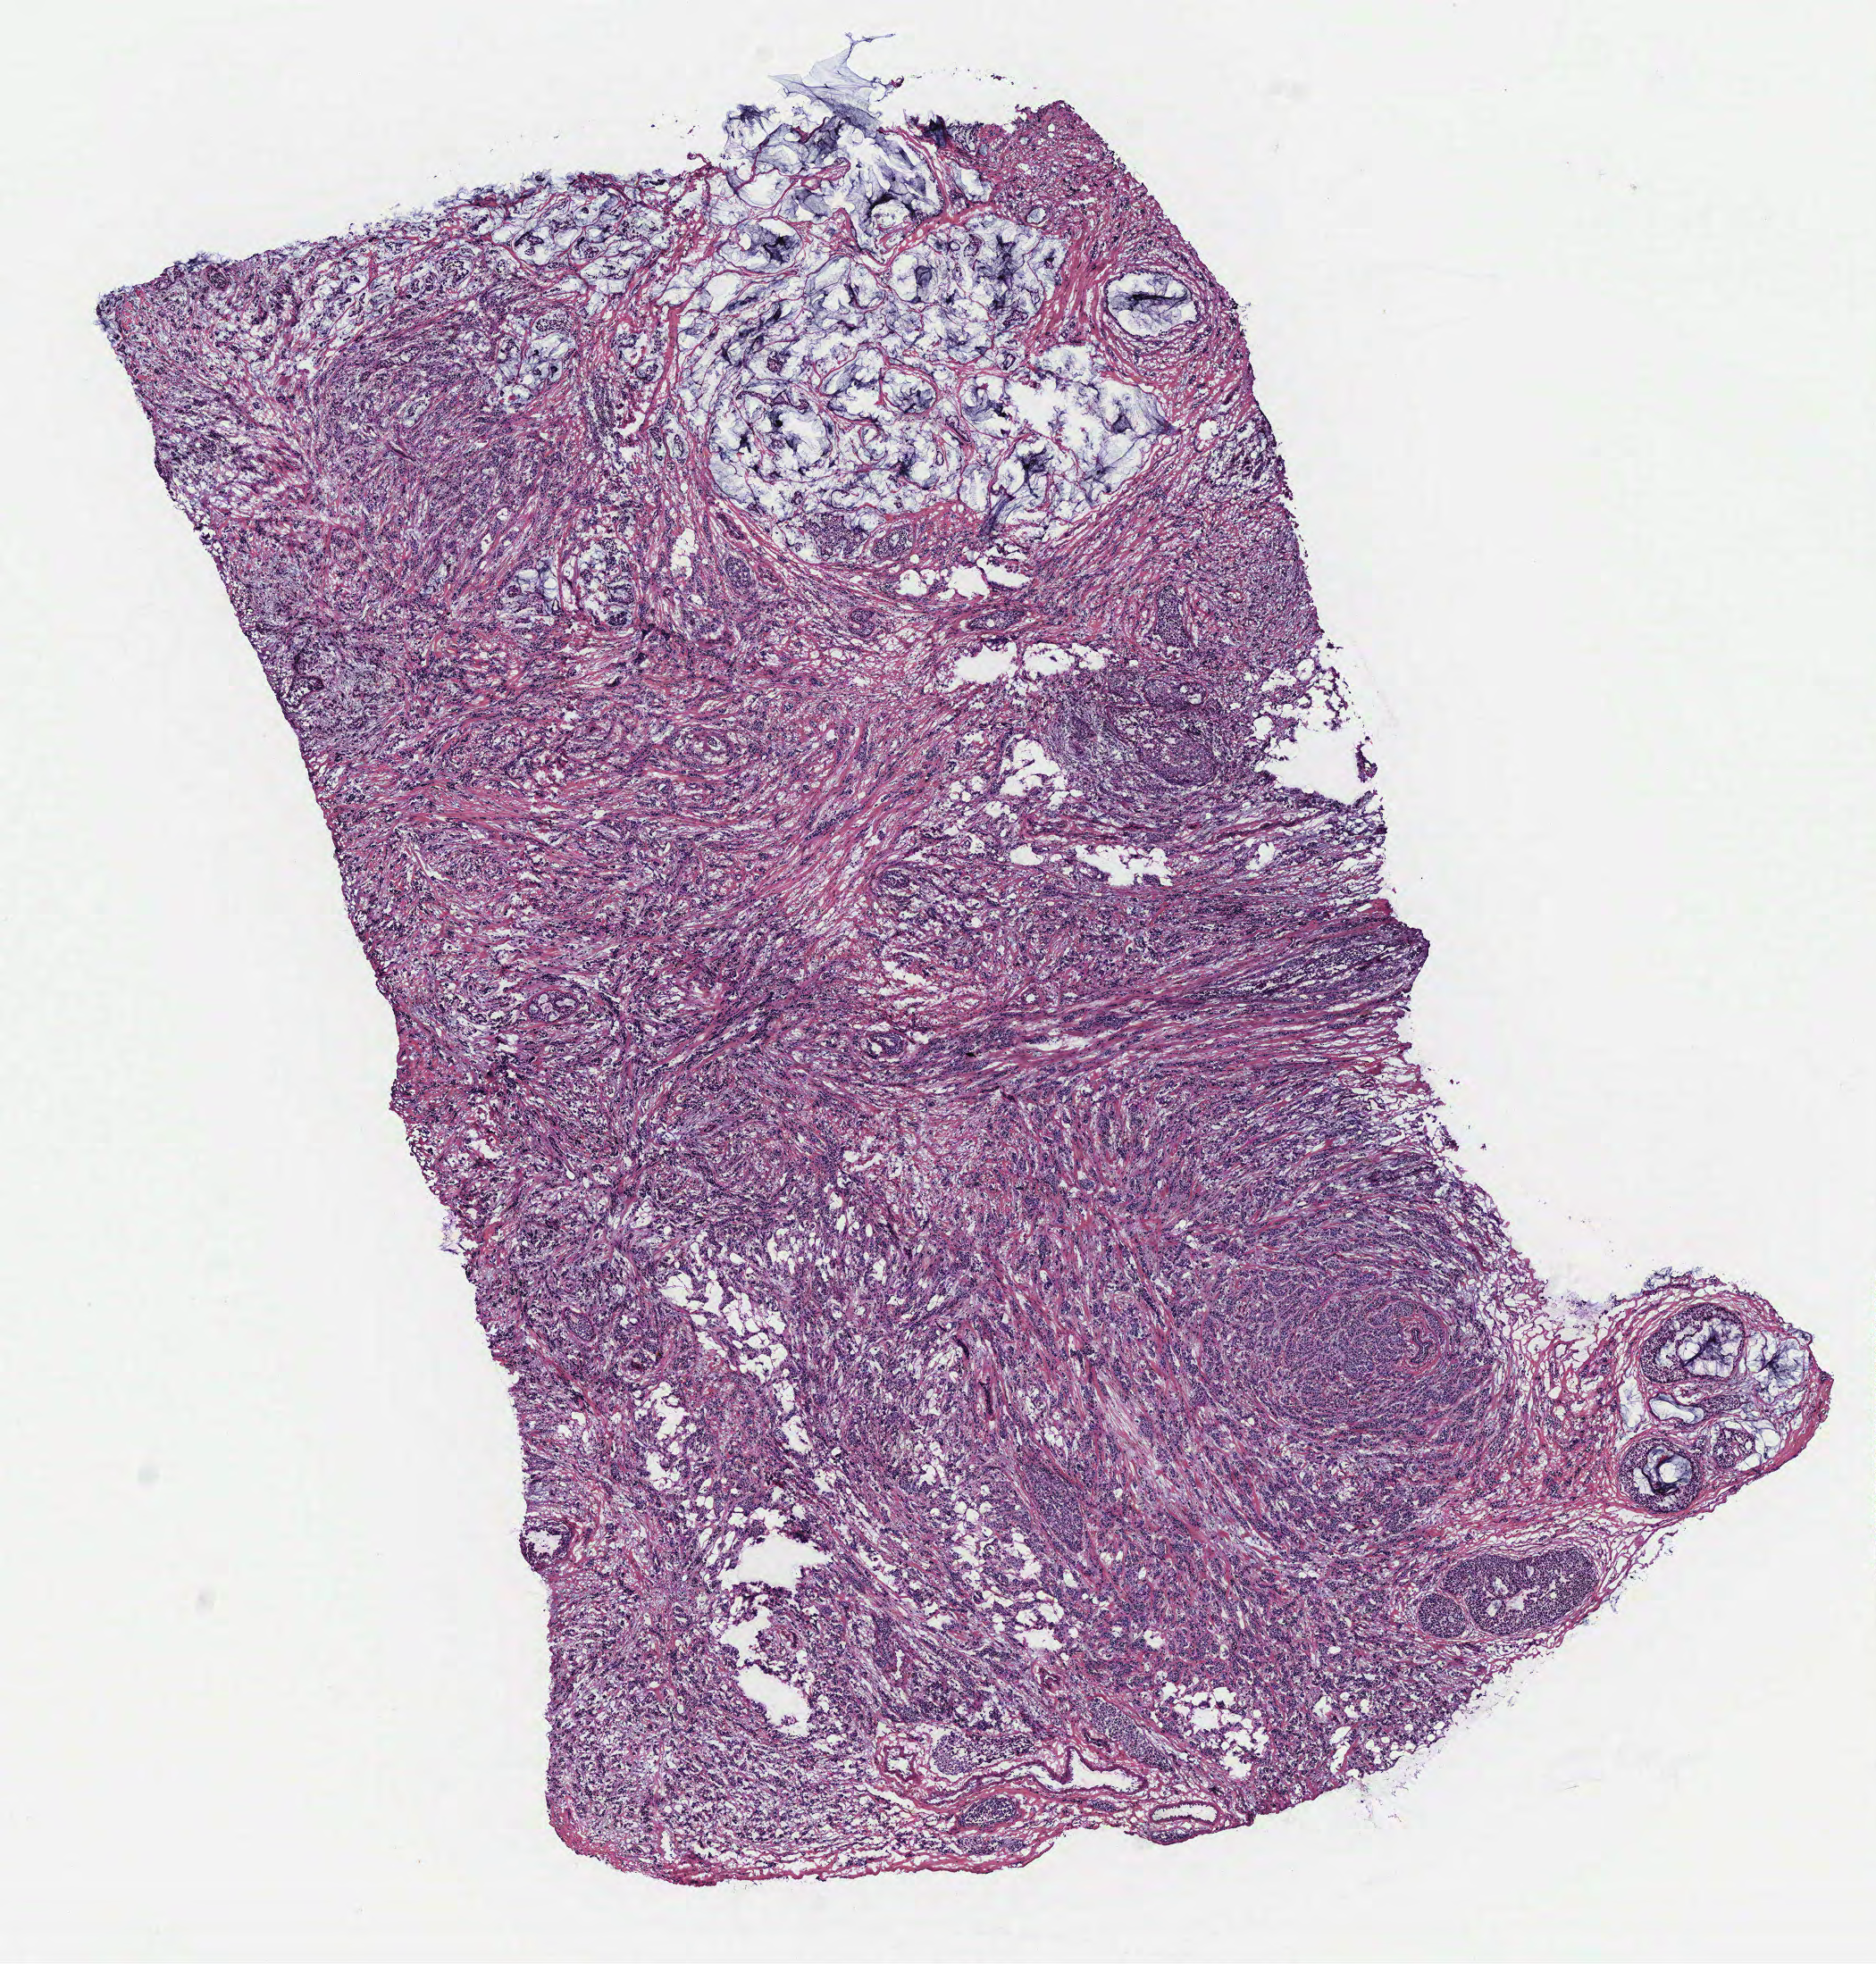
Hematoxylin and eosin (H&E) stained whole-slide image — a low-resolution overview of the entire scanned area, about 8.4 x 8.8 mm. Breast, tumour tissue. 37-year-old female patient.
• AJCC pathologic stage: IIB
• histologic diagnosis: Infiltrating duct carcinoma, NOS